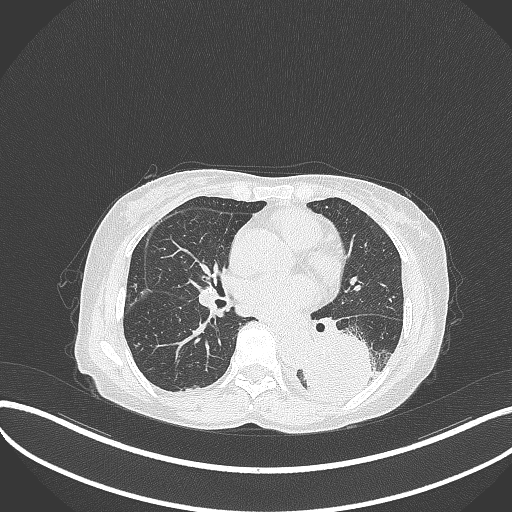
Chest CT, one axial slice. Slice 150 of 370 in the series (ordered by position). 120 kVp. Lung window (W 1500 / L -600 HU). 512 × 512 image matrix, field of view 400 × 400 mm. Female patient, age 78 years. Case-level facts recorded for this patient, not image findings: clinical TNM (as recorded): T3 N0 M1.
Structures marked on this image (bounding box drawn by a radiologist):
- lung tumour (recorded histology: squamous cell carcinoma): bounding box <301,324,390,403> (left, top, right, bottom; pixels)